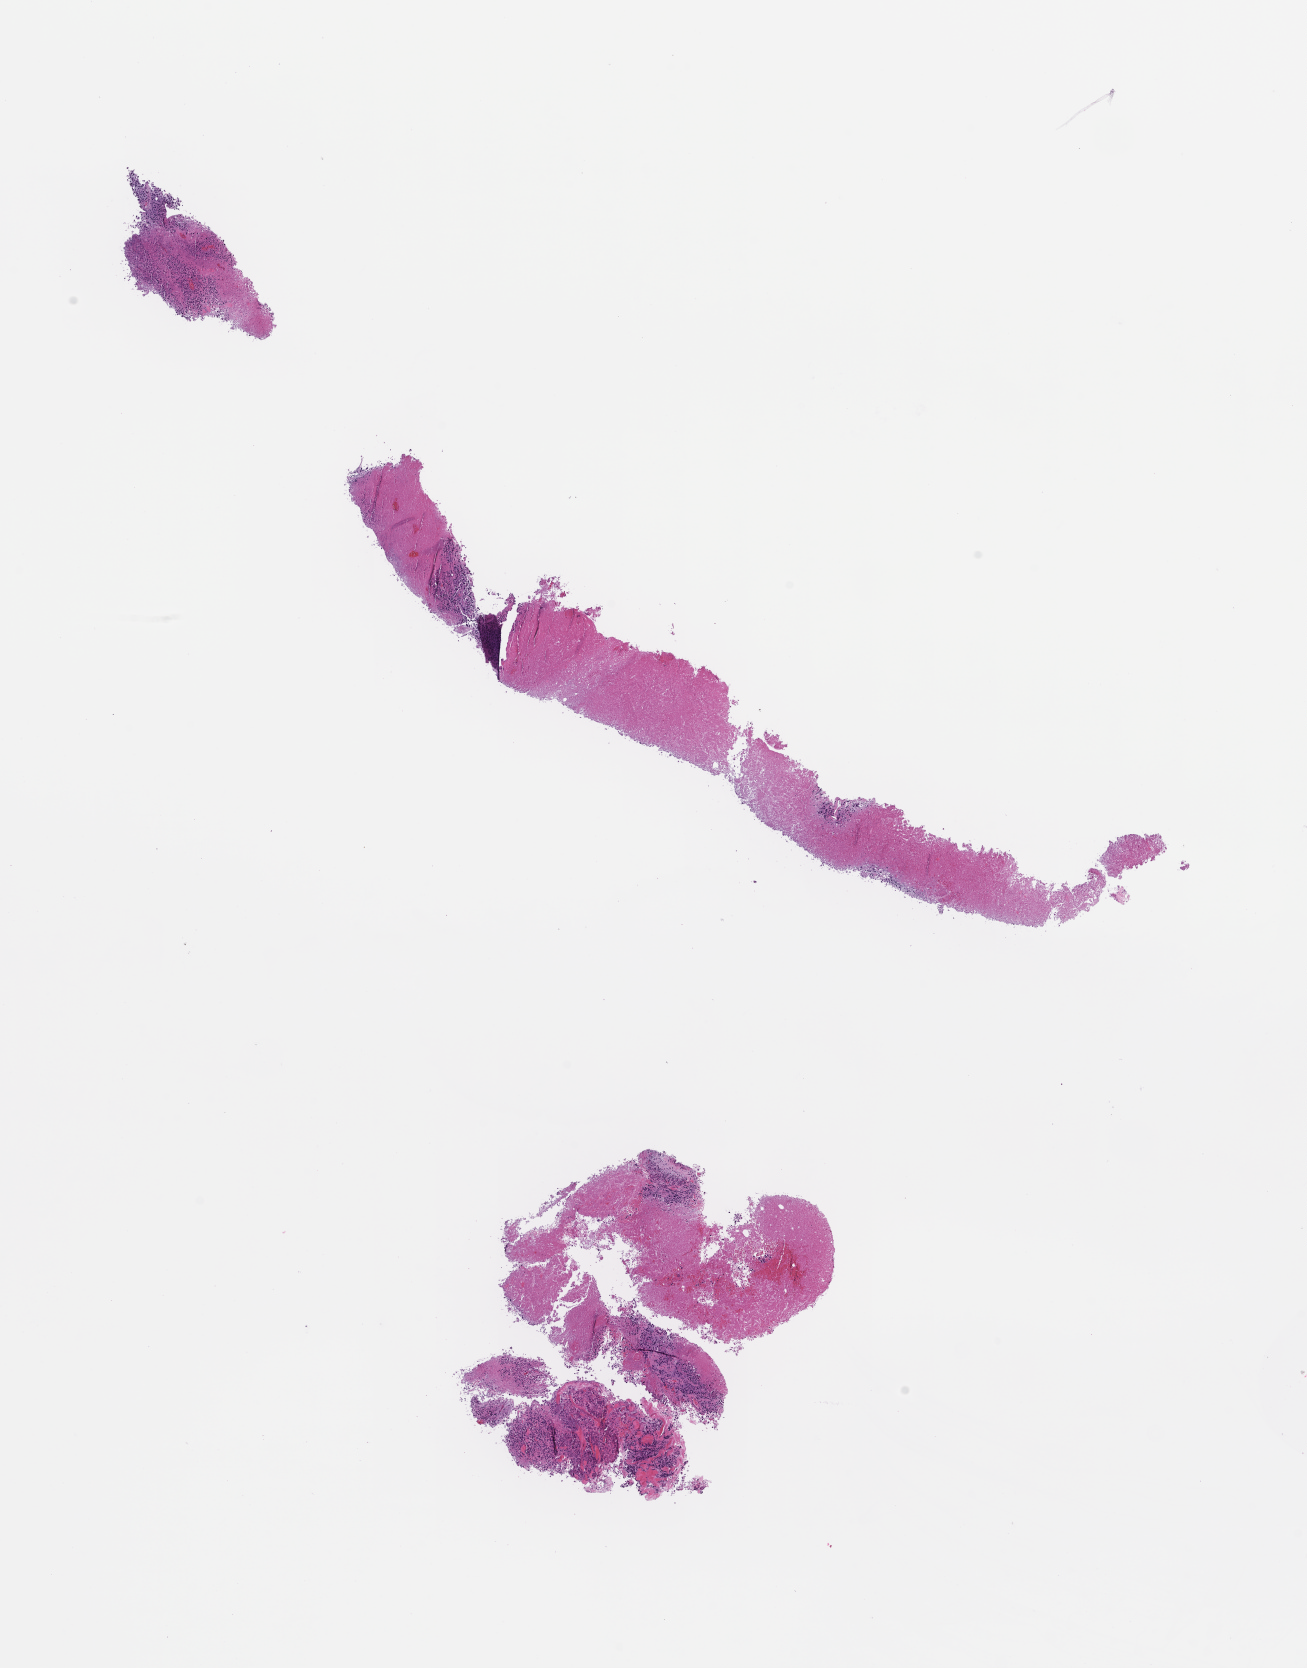
Digitized haematoxylin and eosin-stained section, low-resolution overview of the scanned area, about 10.6 x 13.5 mm. FFPE section. Collected at disease progression. Female patient.
This section: metastasis (sampled organ not recorded). Patient diagnosis (primary): Melanoma.